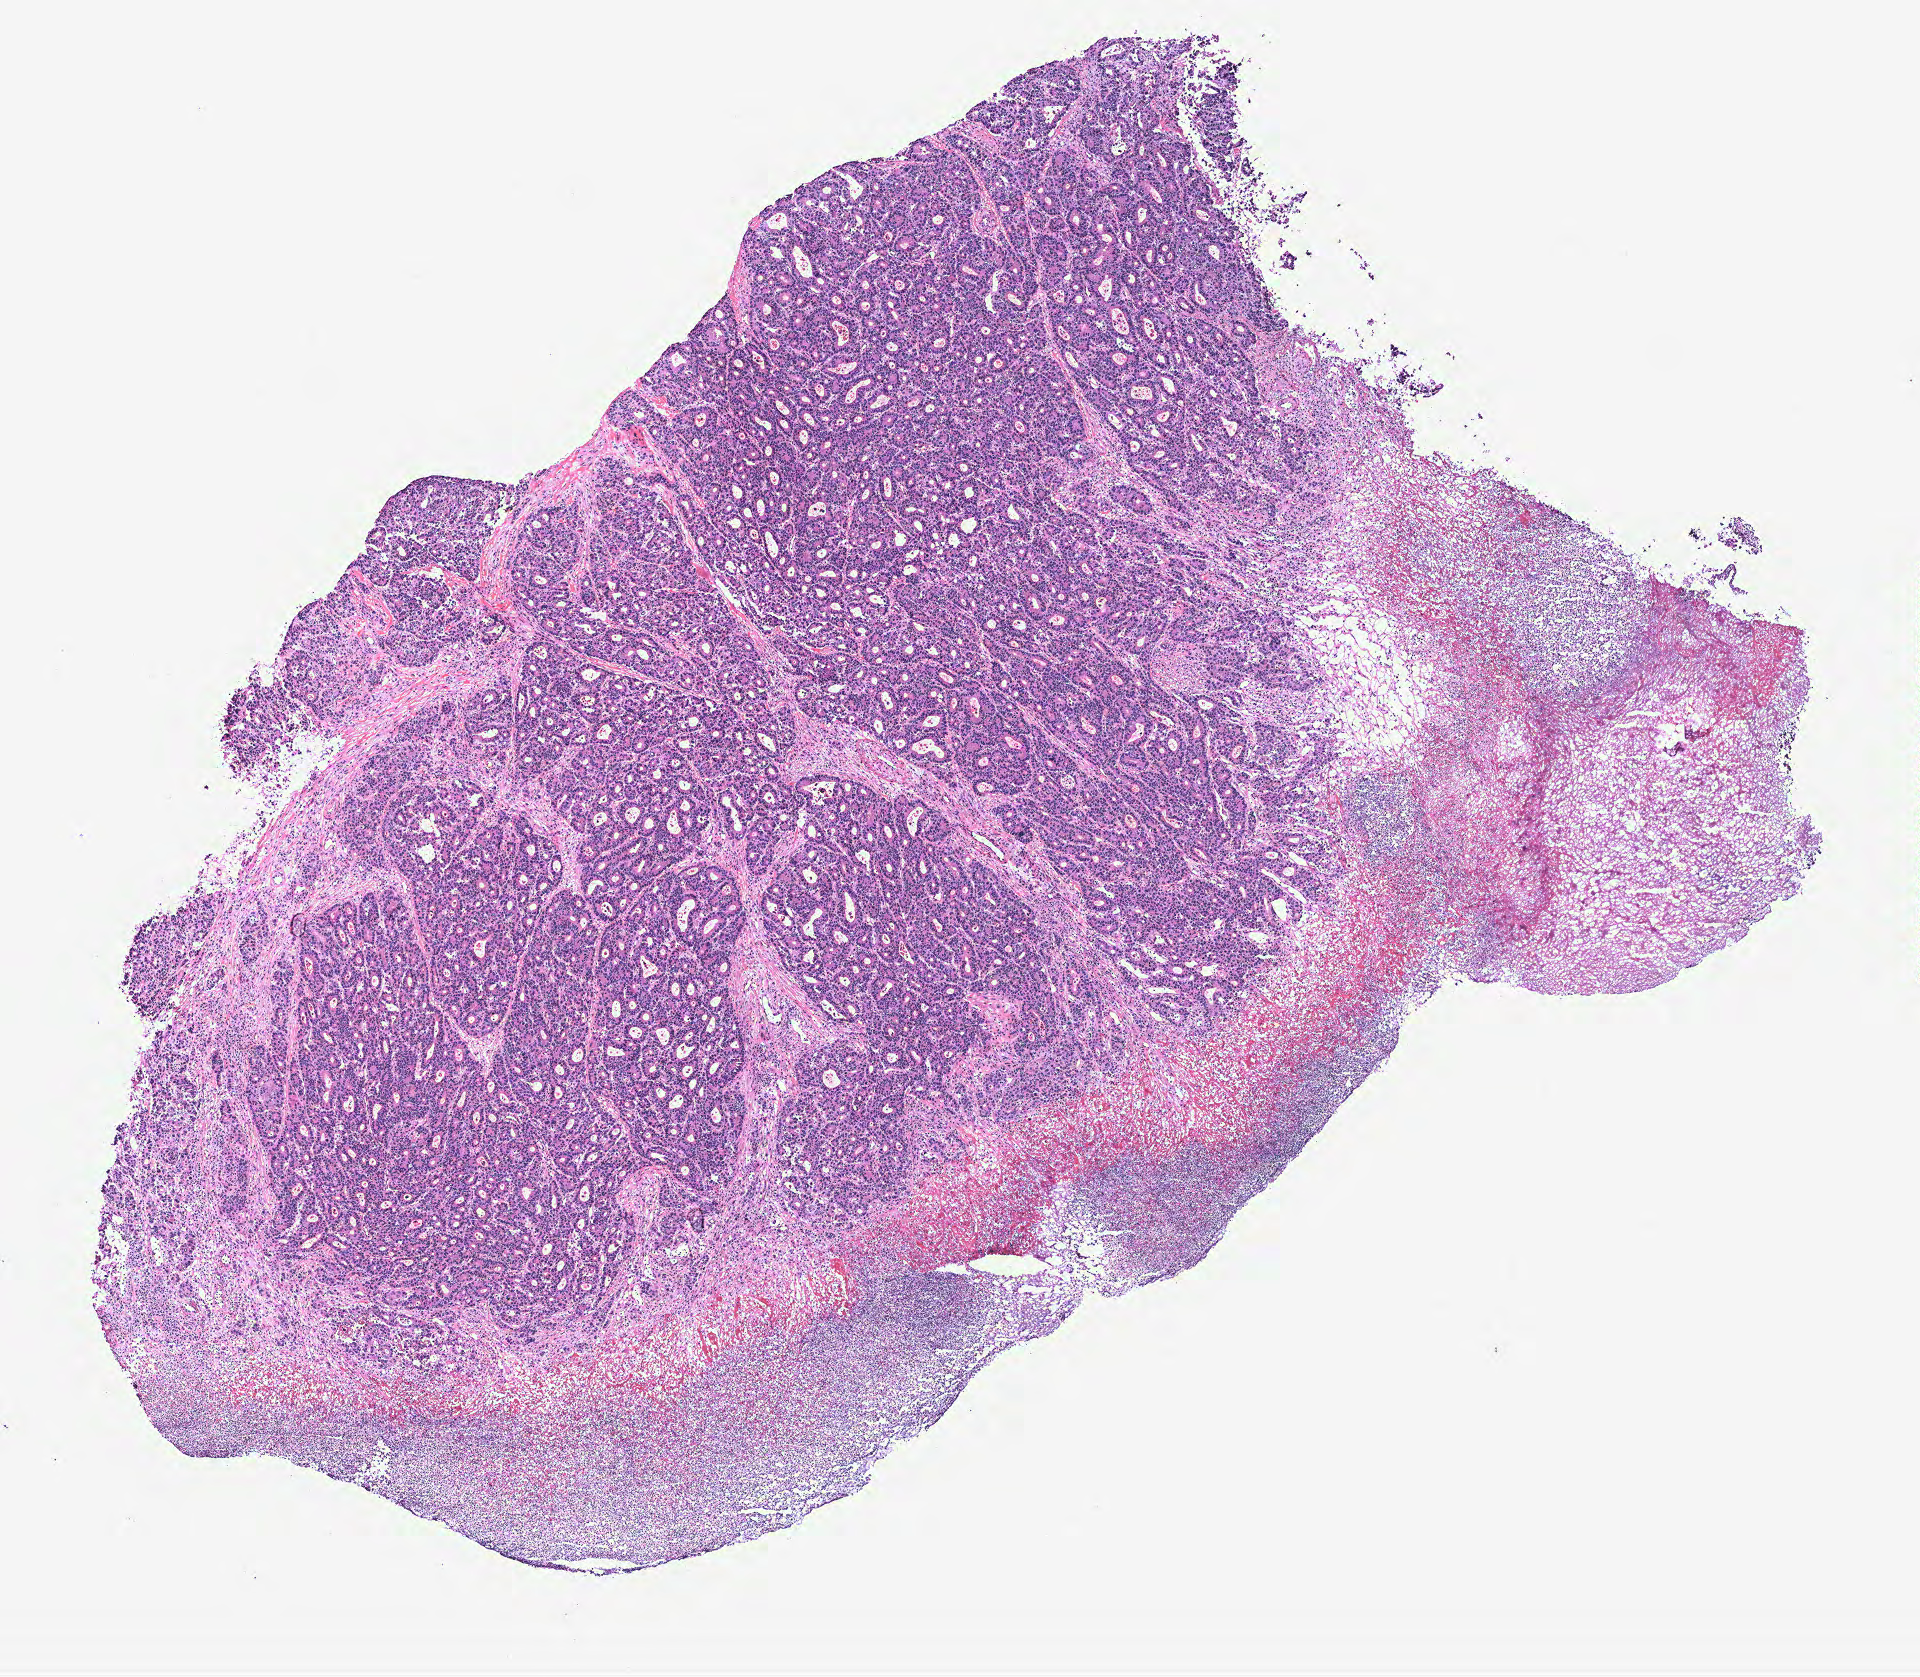
Hematoxylin and eosin (H&E) stained whole-slide image — shown as a low-resolution overview of the whole scanned area (about 7.7 x 6.7 mm, from a 40x scan). Colon, tissue type not recorded.
Patient diagnosis (cohort enrolment): colon cancer (colon).